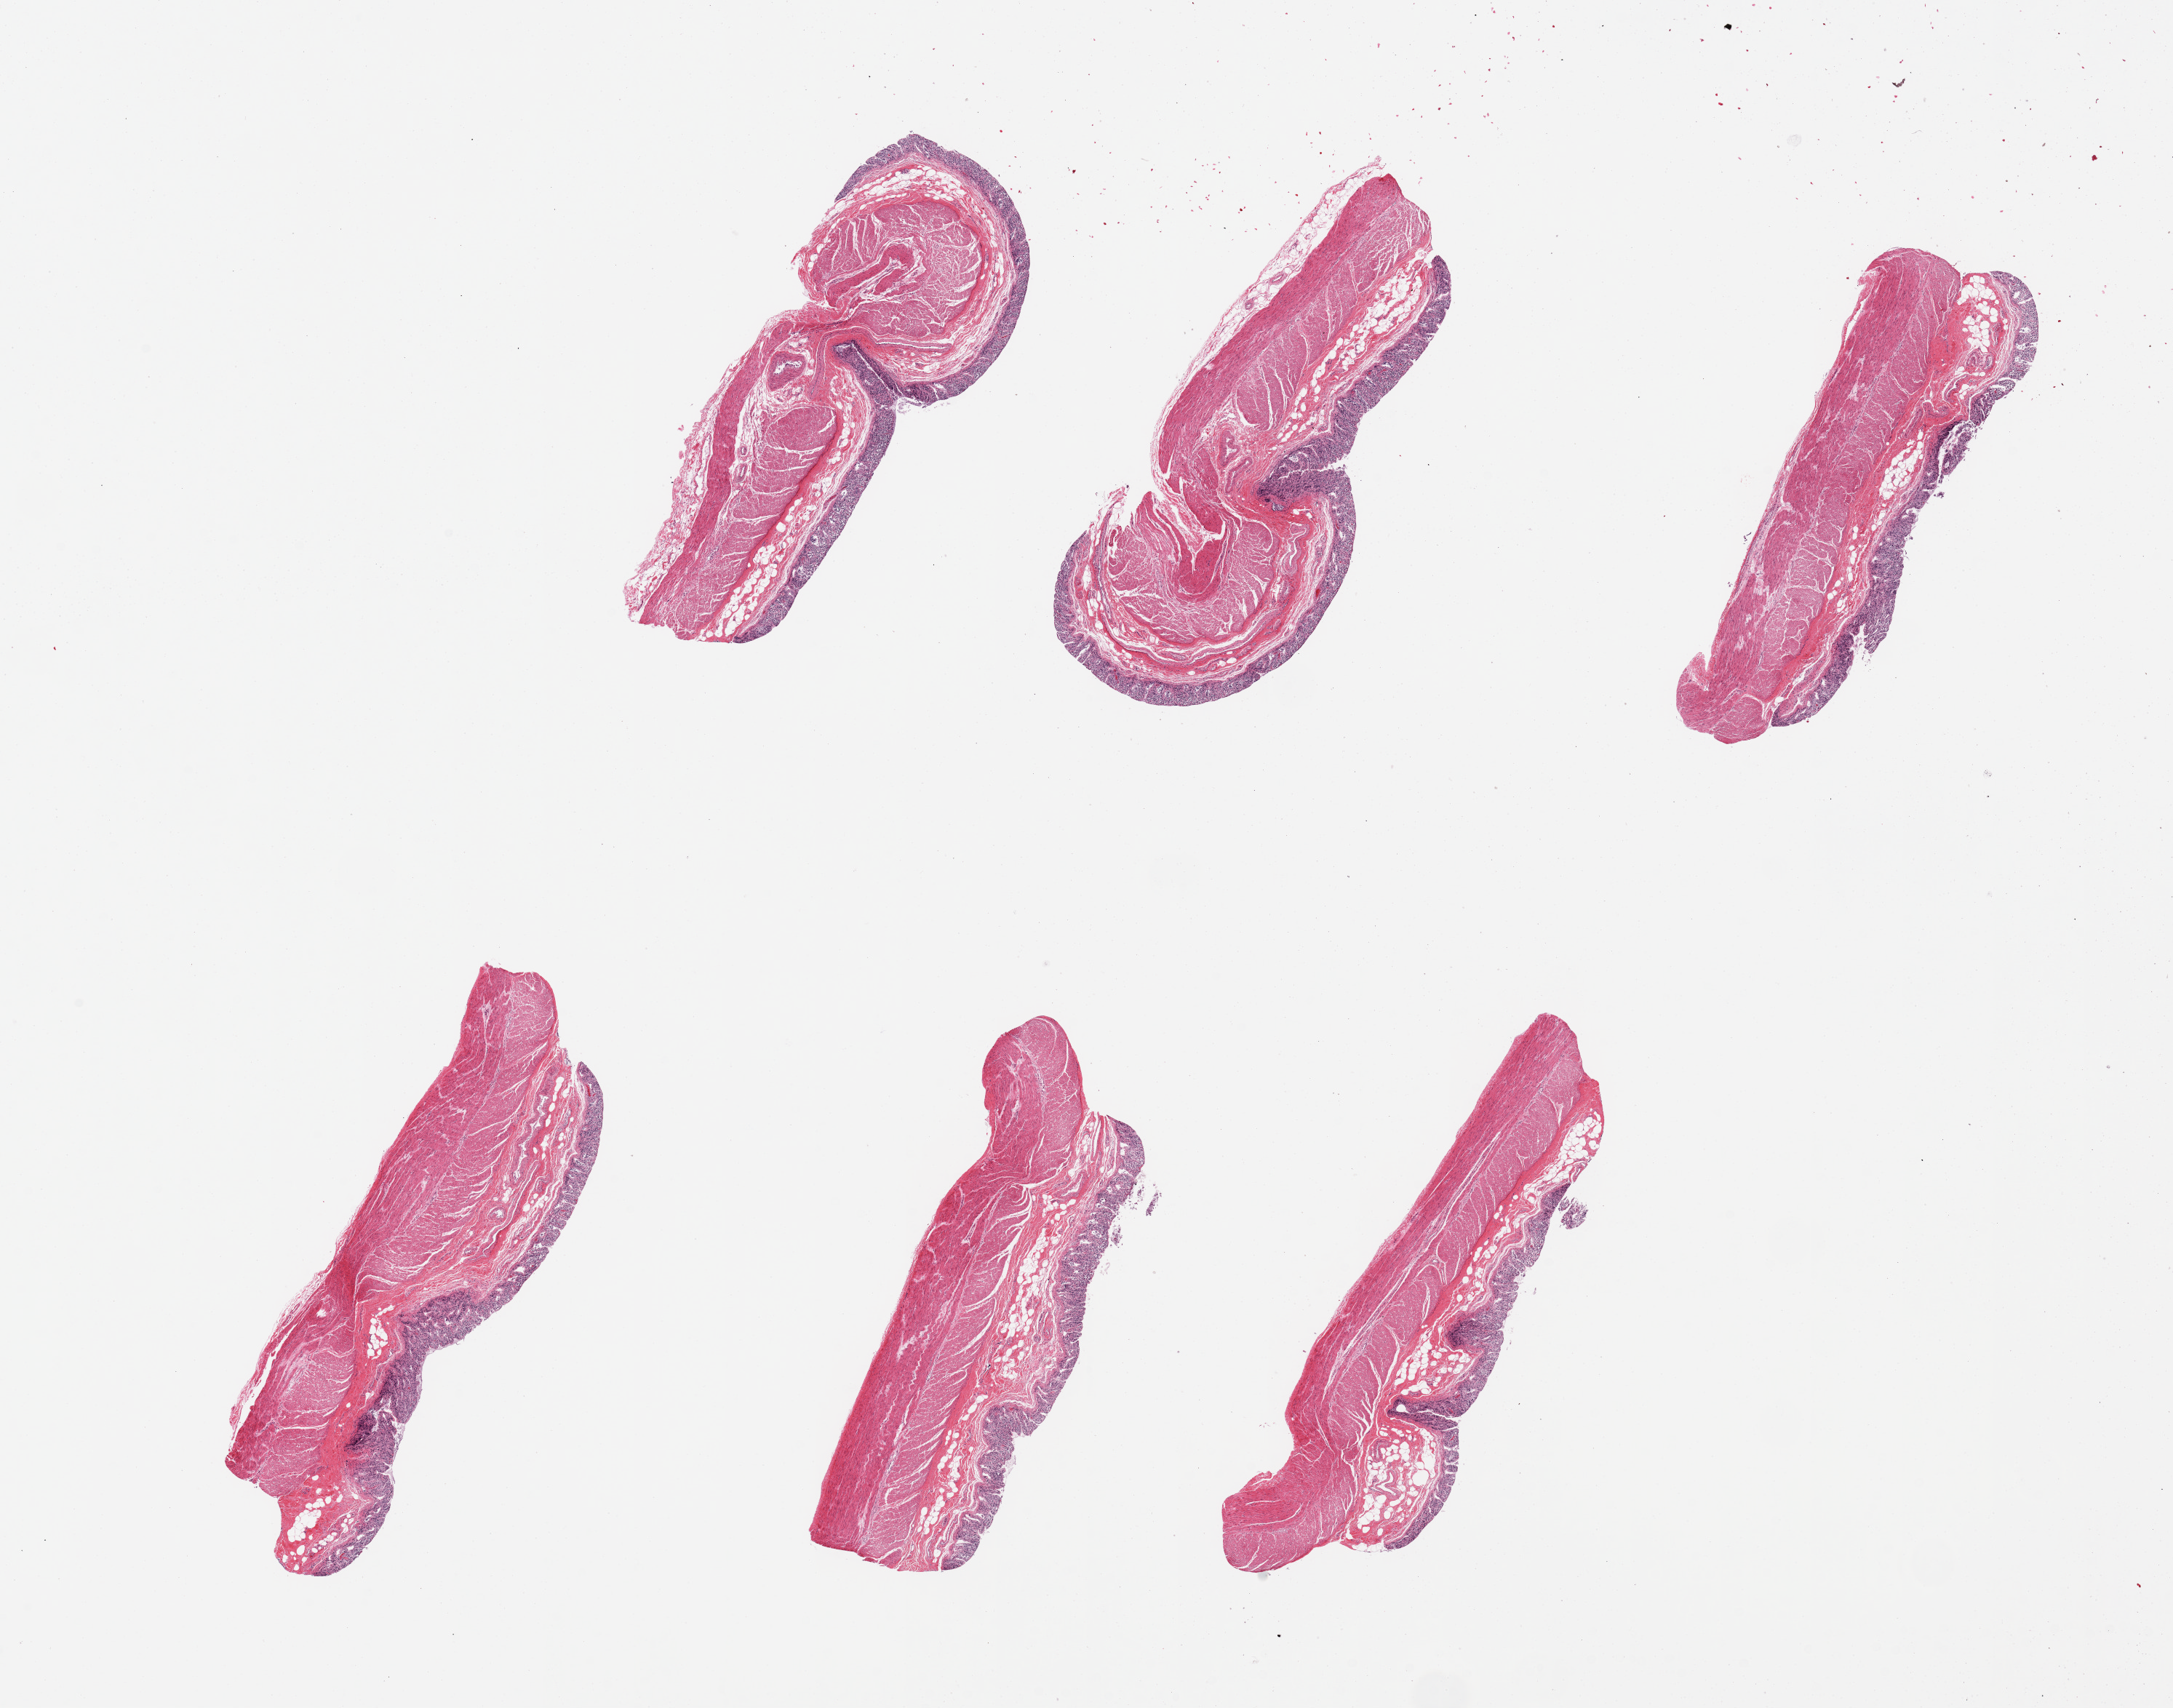
Digitized hematoxylin and eosin (H&E)-stained section — low-resolution overview of the scanned area, about 23.6 x 18.6 mm (acquisition: 20x scan); PAXgene-fixed paraffin-embedded (PFPE) section; sampled site (target tissue): transverse colon; tissue donor sample. Donor sex: male.
Review note (as recorded): 6 pieces. mucosa severly autolyzed; muscularis preserved.